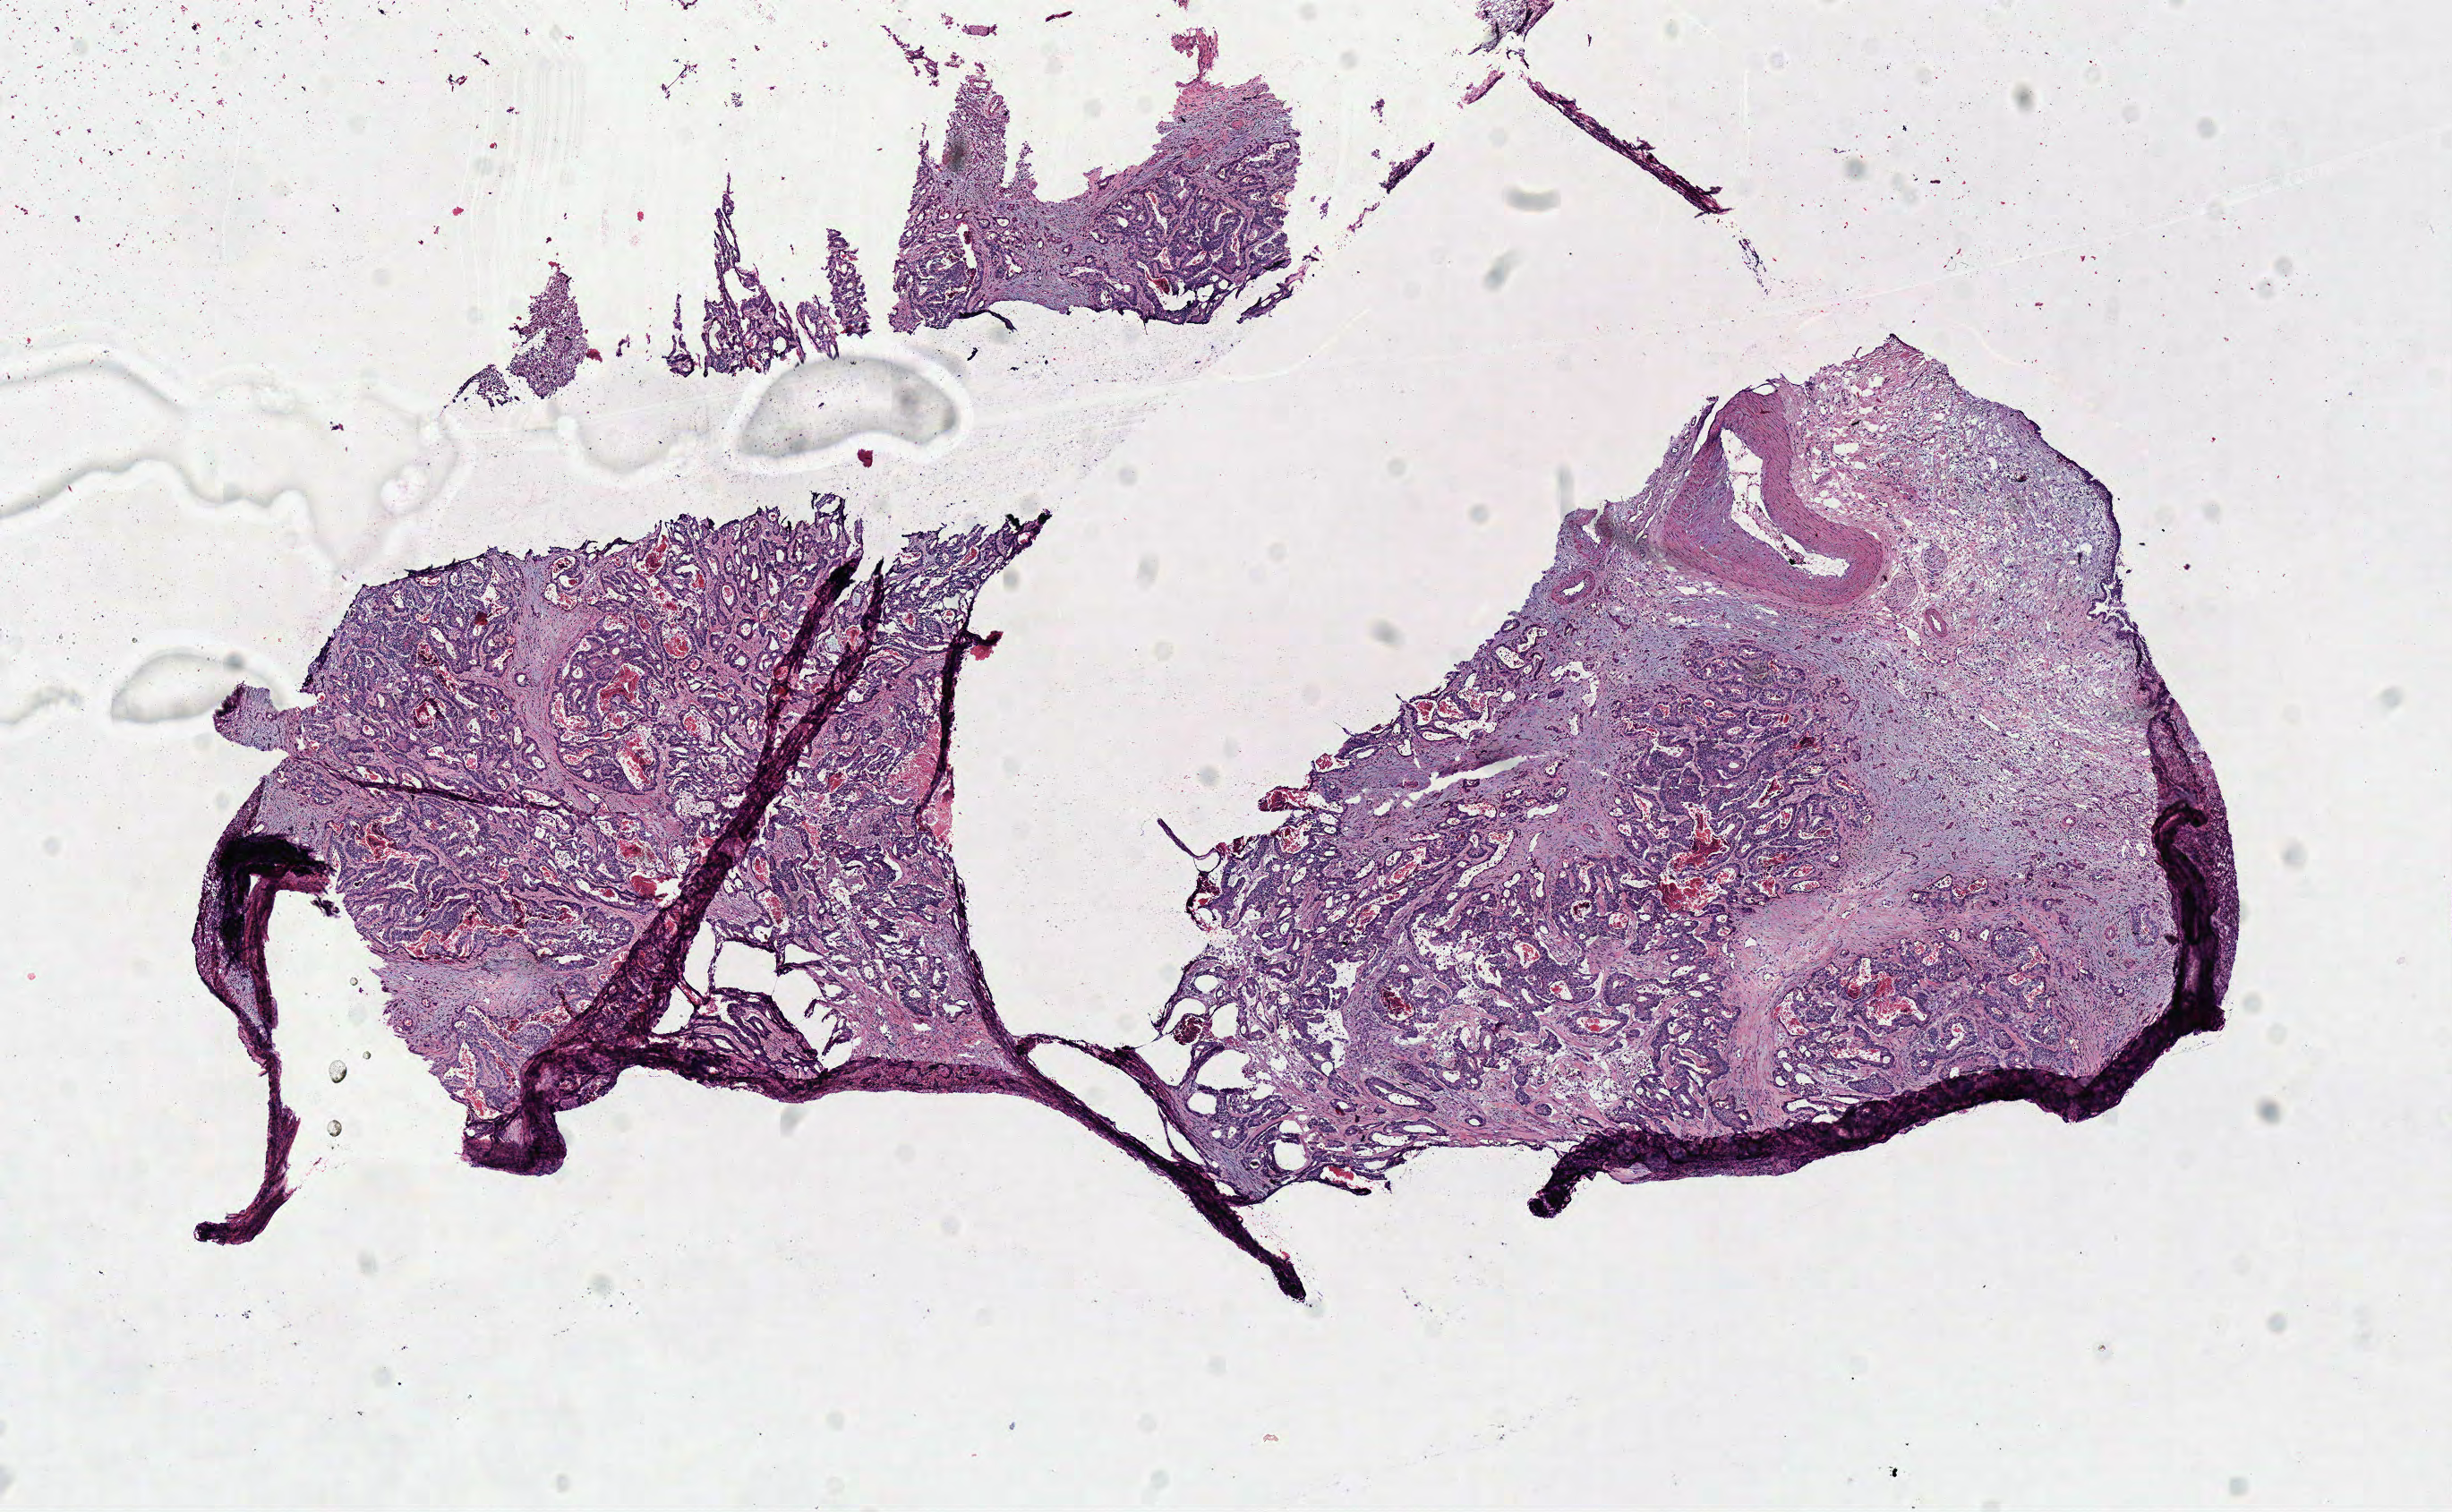
Digitized H&E-stained tissue section (whole slide) — whole scanned area (about 10.8 x 6.6 mm, from a 40x scan) shown as a low-resolution overview, frozen section from the top of the tissue portion, sample: recurrent tumour, colon. Patient: female, age at initial diagnosis 51 years. Slide review estimates, as recorded: tumour cells 60%, tumour nuclei 80%, normal cells 0%, stromal cells 30%, necrosis 10%.
* this section: recurrent tumour
* patient diagnosis: Adenocarcinoma, NOS (sigmoid colon)